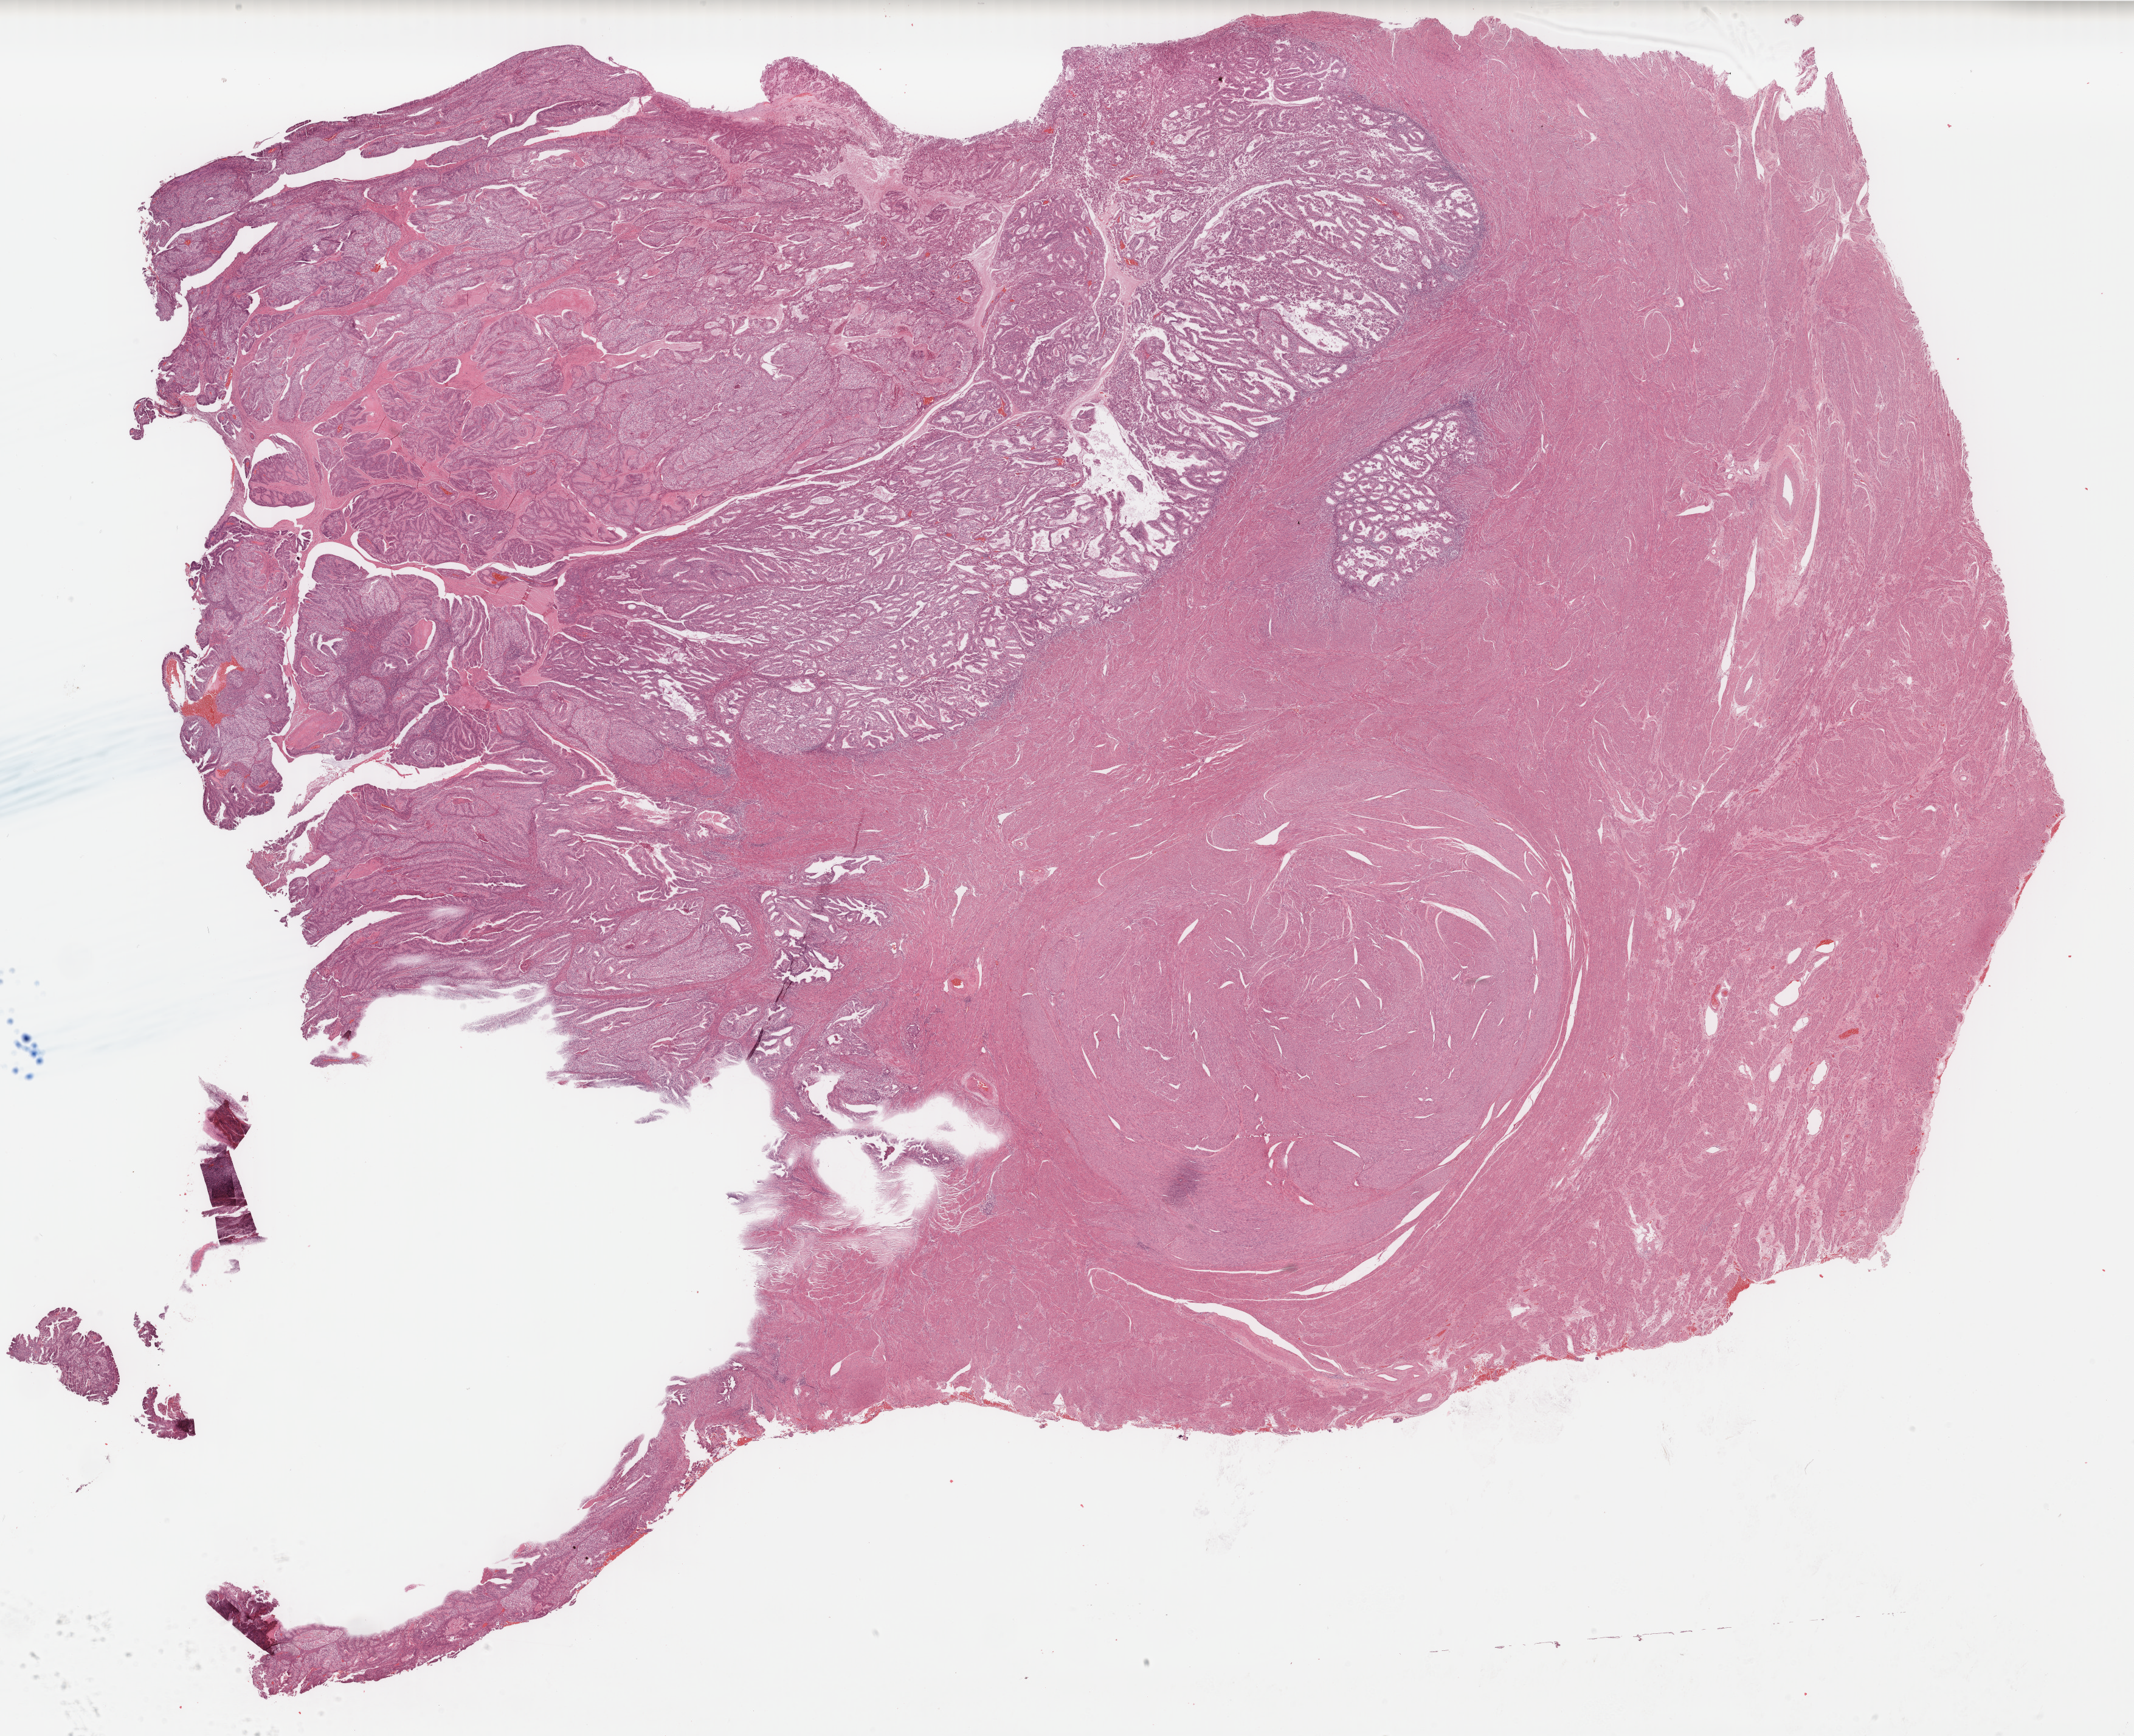
Whole-slide histology image, H&E — shown as a low-resolution overview of the whole scanned area (about 27.9 x 22.7 mm); FFPE section; primary tumour sample from the uterus. Patient: female, age at initial diagnosis 63 years. Histologic grade: G2 (moderately differentiated).
* FIGO stage: IC
* pathologic diagnosis: Endometrioid adenocarcinoma, NOS (endometrium)